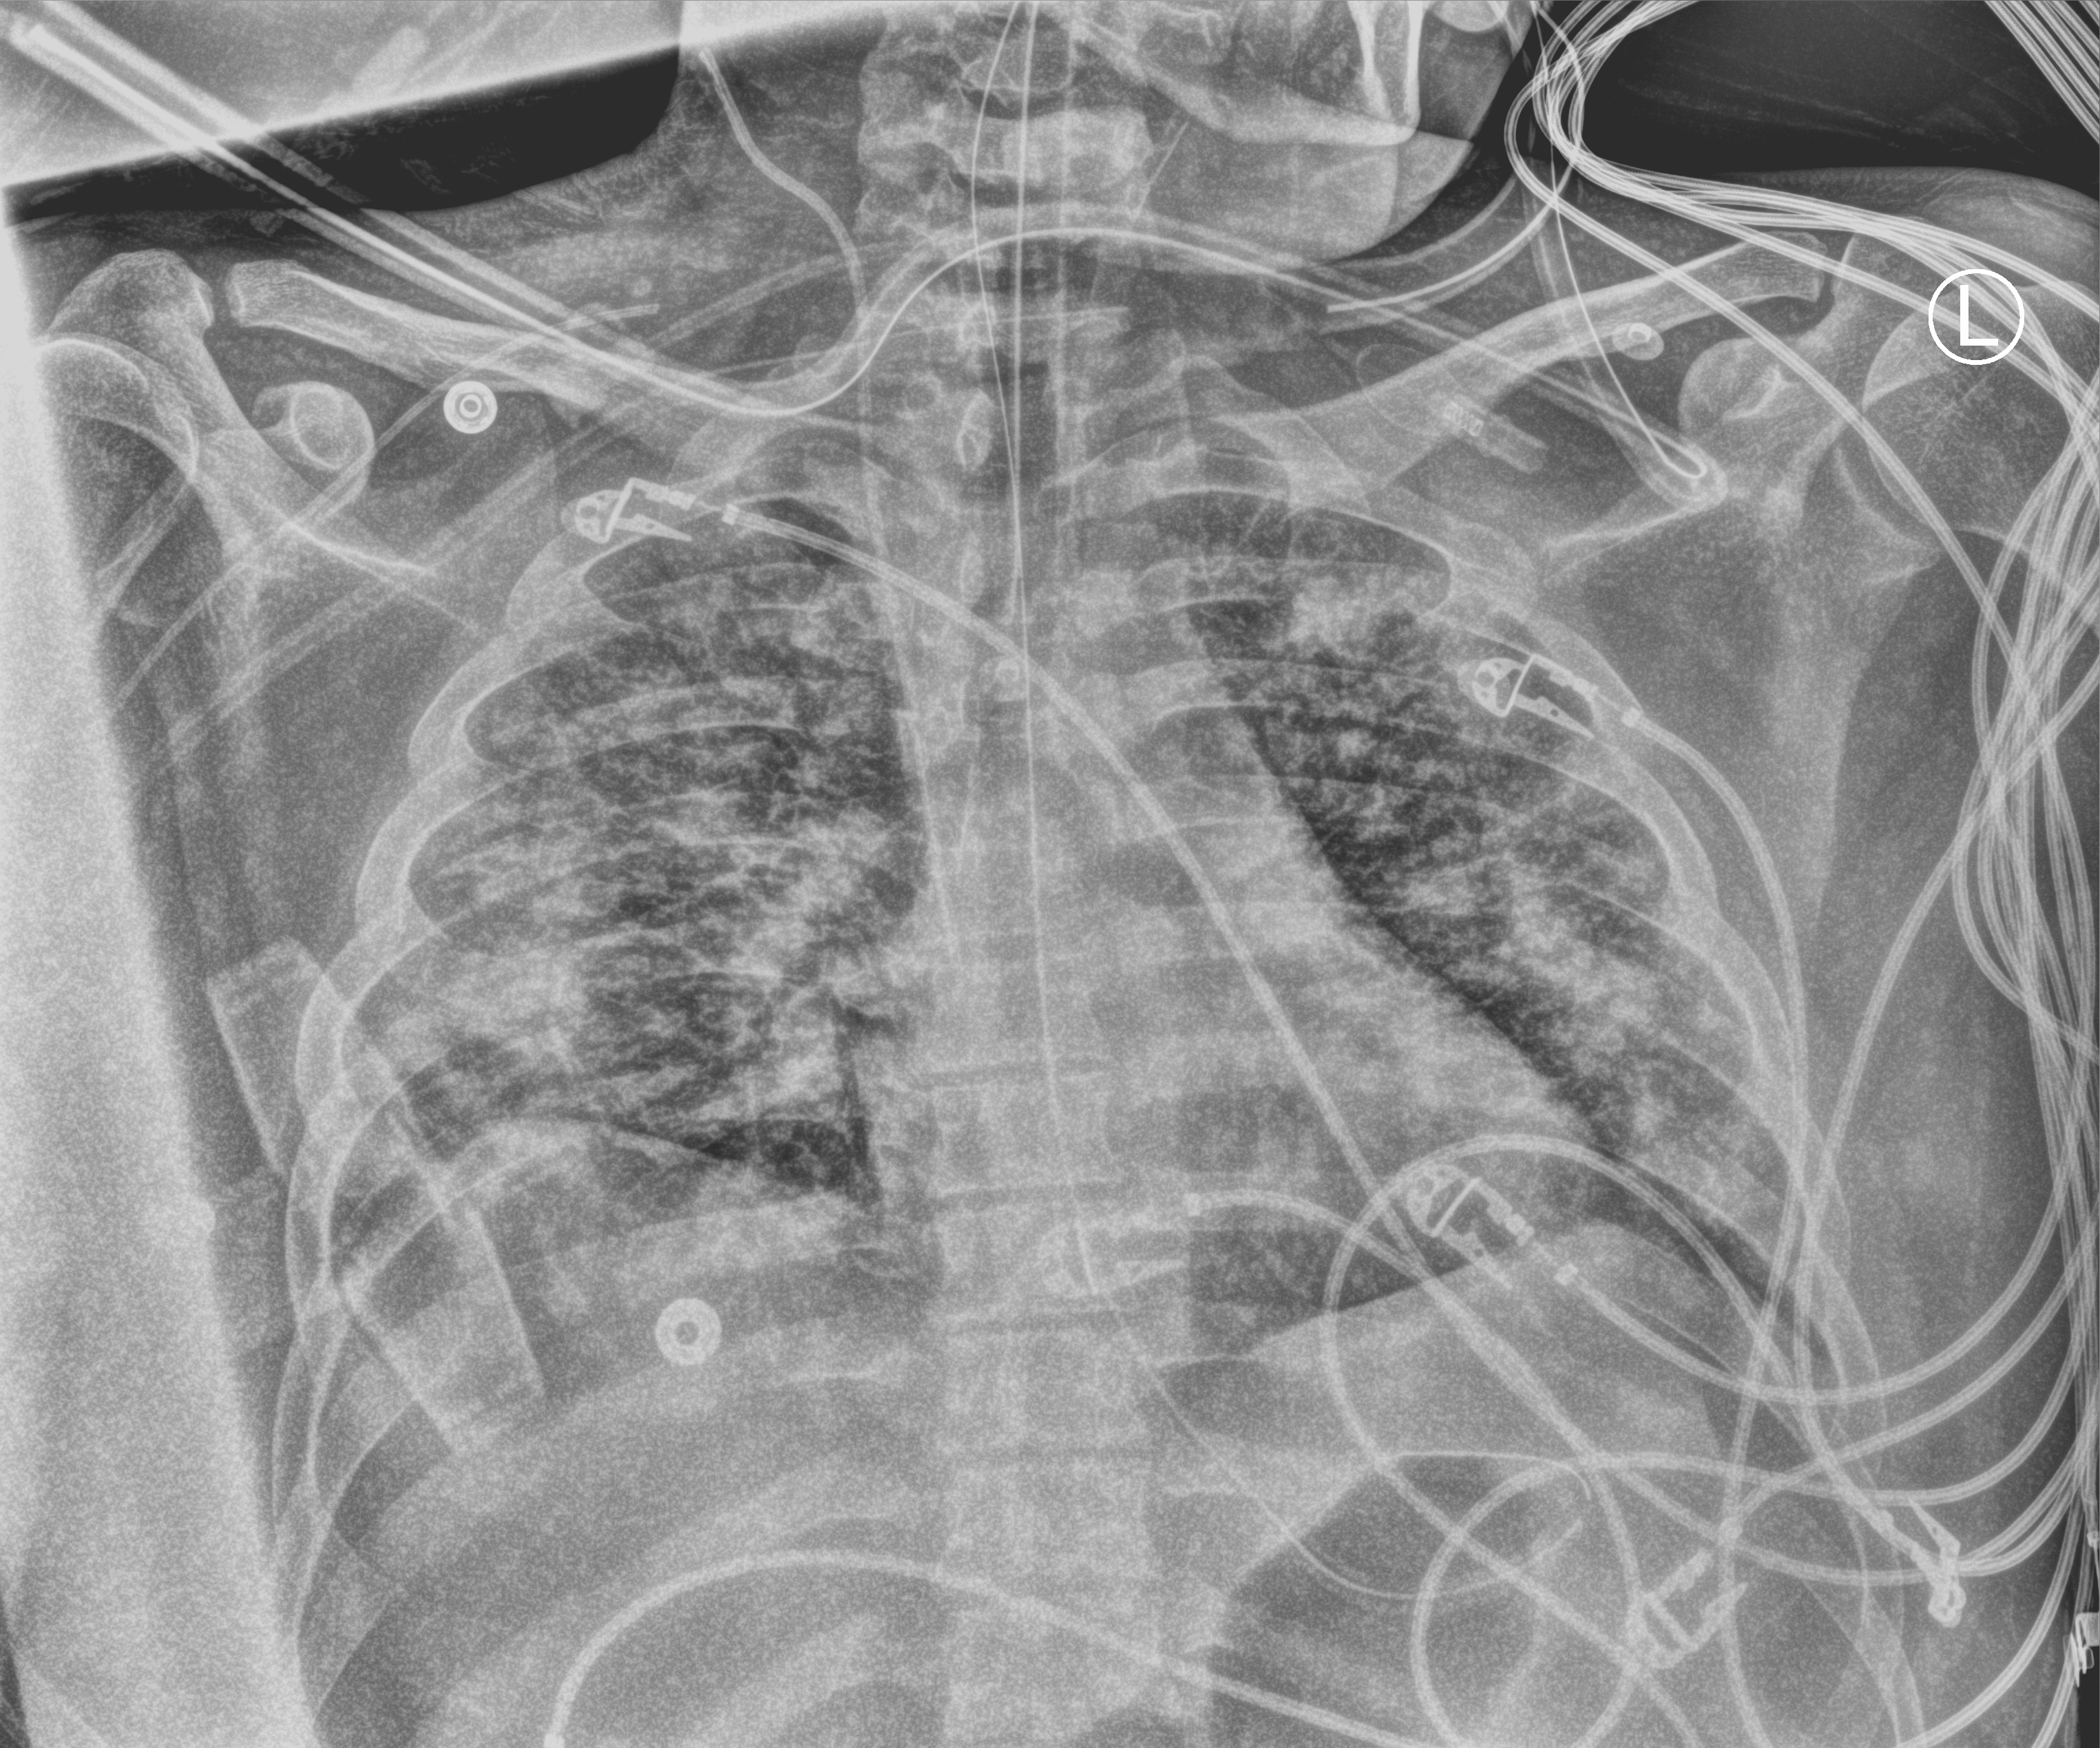
Bedside chest radiograph (computed radiography); anteroposterior (AP) projection. Patient hospitalised with COVID-19; male, aged 18–59 years.
Admission-level facts for this patient (not findings on this image; timing relative to this image not recorded): mechanically ventilated during this hospital stay: yes; other chronic lung disease (admission record): no; admitted to intensive care during this hospital stay: yes.